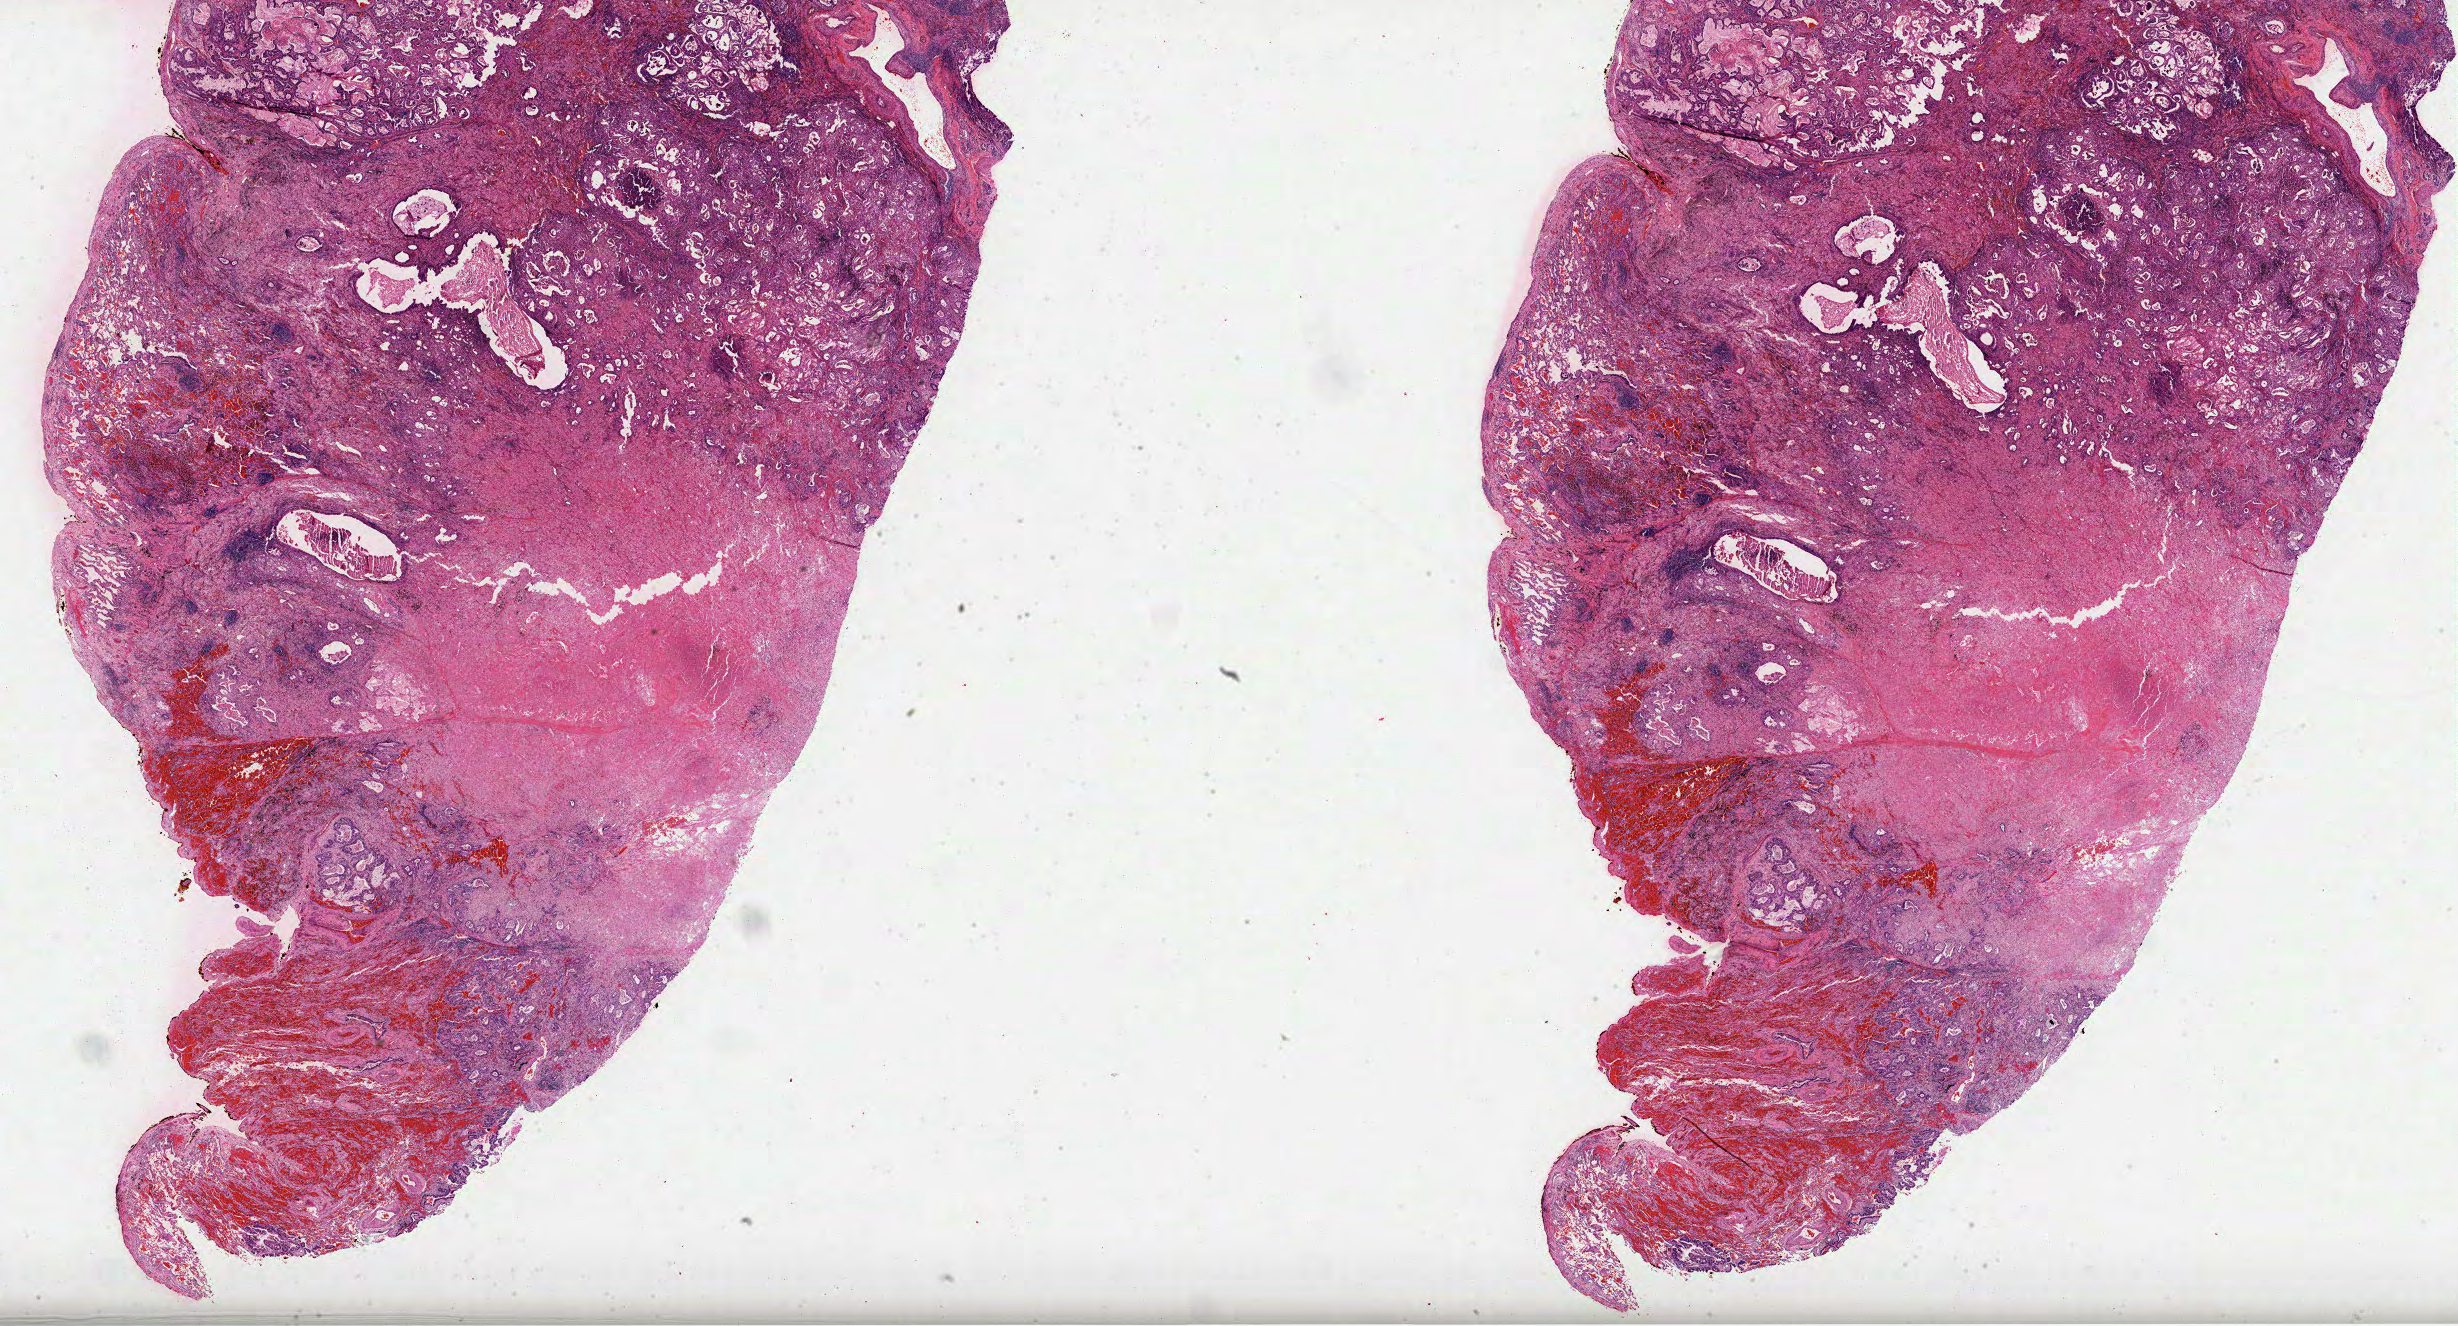
Digitized Hematoxylin and eosin (H&E) stained tissue section (whole slide), a low-resolution overview of the entire scanned area, about 39.6 x 21.4 mm (slide scanned at 40x); formalin-fixed paraffin-embedded (FFPE) diagnostic section; primary tumour sample from the lung. Male, age 70 years at initial diagnosis.
- pathologic diagnosis: Mucinous adenocarcinoma
- AJCC pathologic stage: IIA